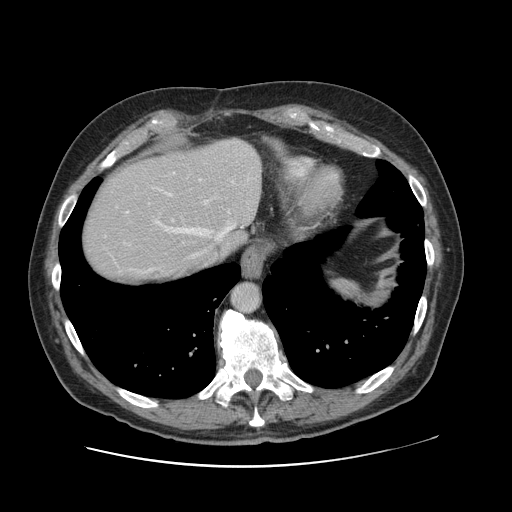
Contrast-enhanced abdominal CT, one axial slice. 120 kVp. Soft-tissue window (W 400 / L 40 HU). 2.5 mm slice thickness. 512 × 512 image matrix, field of view 402 × 402 mm. Male patient, age 71 years. From the clinical record (not read from this slice): diagnosis: colorectal cancer liver metastases, imaged before liver resection; multiple liver metastases: no; largest metastasis: 3.3 cm; chemotherapy before resection: no.
Structures marked on this image (manually delineated by an expert):
- hepatic veins: bounding box <155,212,235,266> (left, top, right, bottom; pixels)
- liver: <82,139,261,286>
- planned liver remnant (the part of the liver to remain after resection): <82,162,224,285>